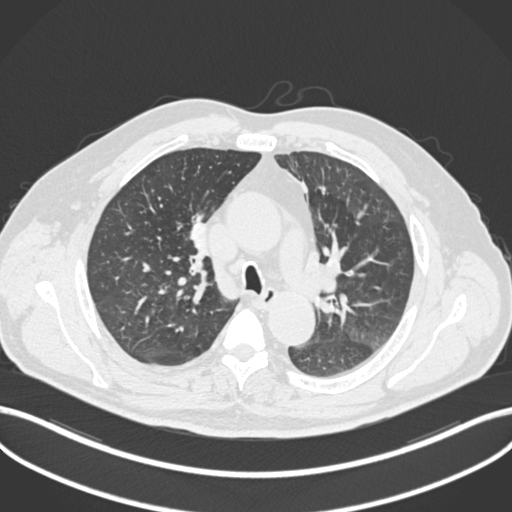
Chest CT, one axial slice. Slice 130 of 255 in the series (ordered by position). Reconstruction kernel B30f. 120 kVp. Lung window (W 1500 / L -600 HU). 512 × 512 image matrix, field of view 400 × 400 mm. Male patient, age 60 years. From the clinical record (not read from this slice): clinical TNM (as recorded): T1b N1 M0.
Structures marked on this image (rectangle marked by the reading radiologist):
- lung tumour (recorded histology: squamous cell carcinoma): box from (x=183, y=207) to (x=220, y=271) px